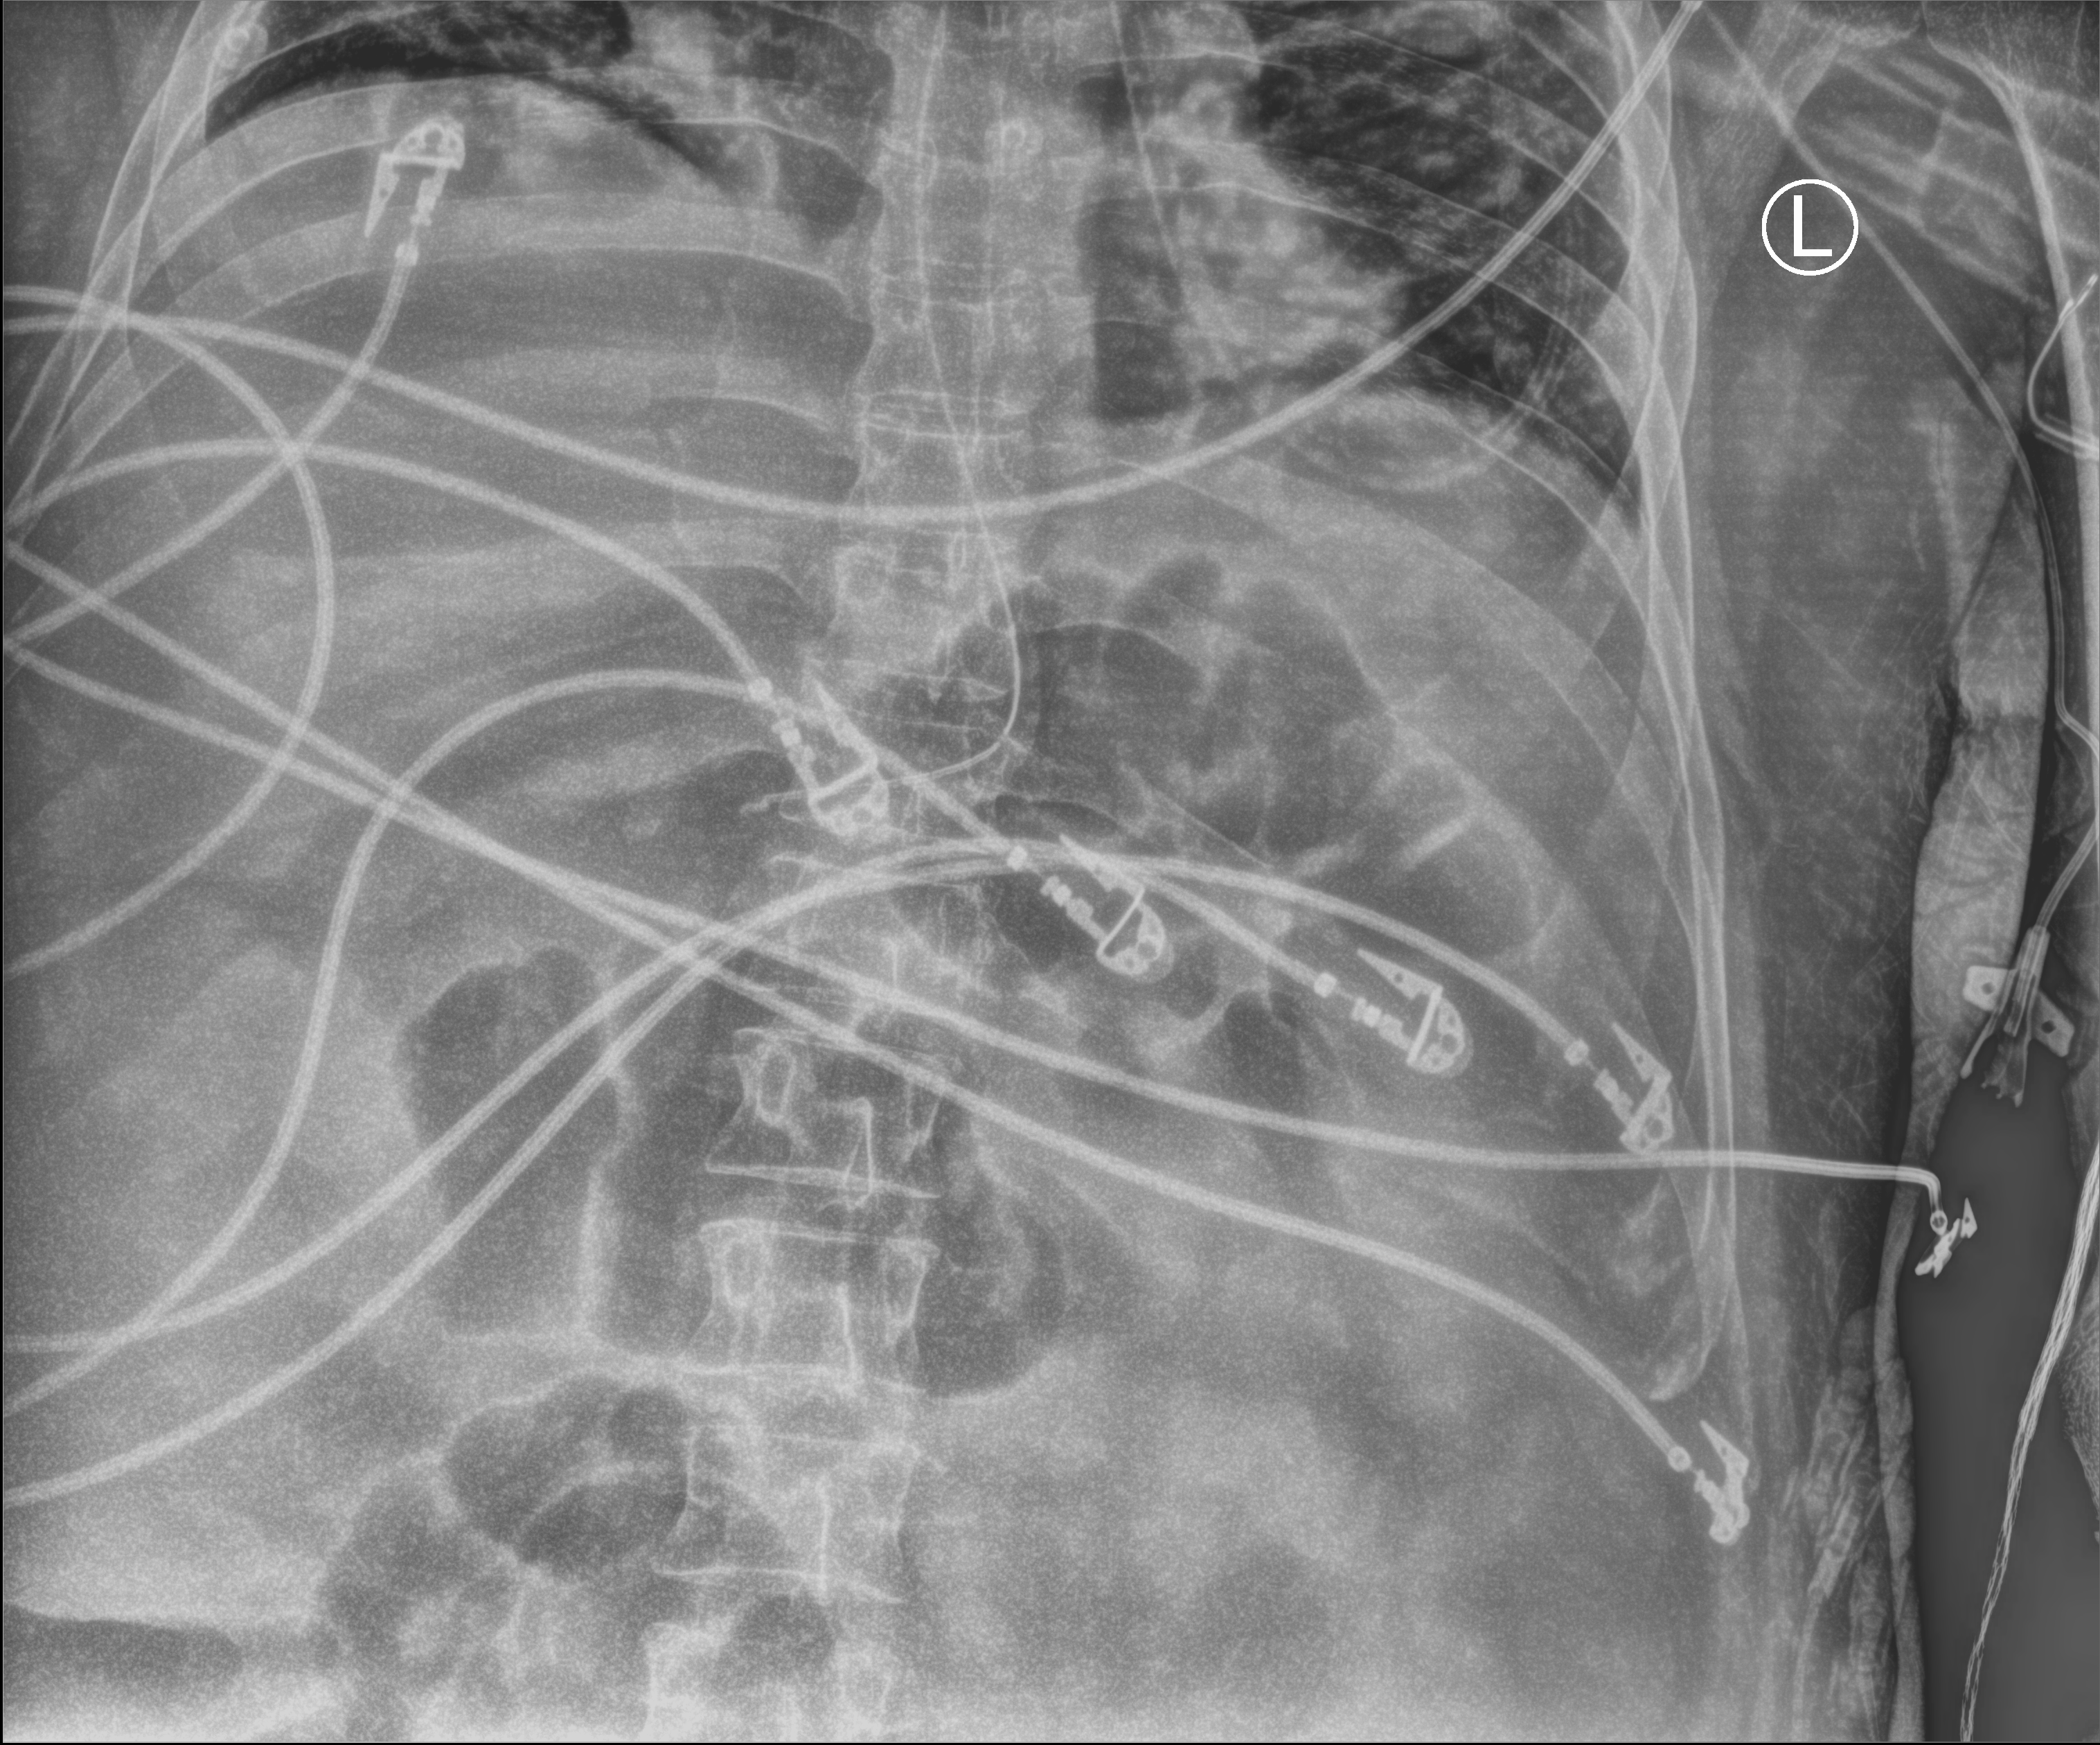
Bedside abdomen radiograph (computed radiography); anteroposterior (AP) projection. Adult patient hospitalised with COVID-19, age 18–59 years.
From the hospital-stay record, not from the radiograph (when in the stay this image was taken is not recorded):
- mechanically ventilated during this hospital stay: yes